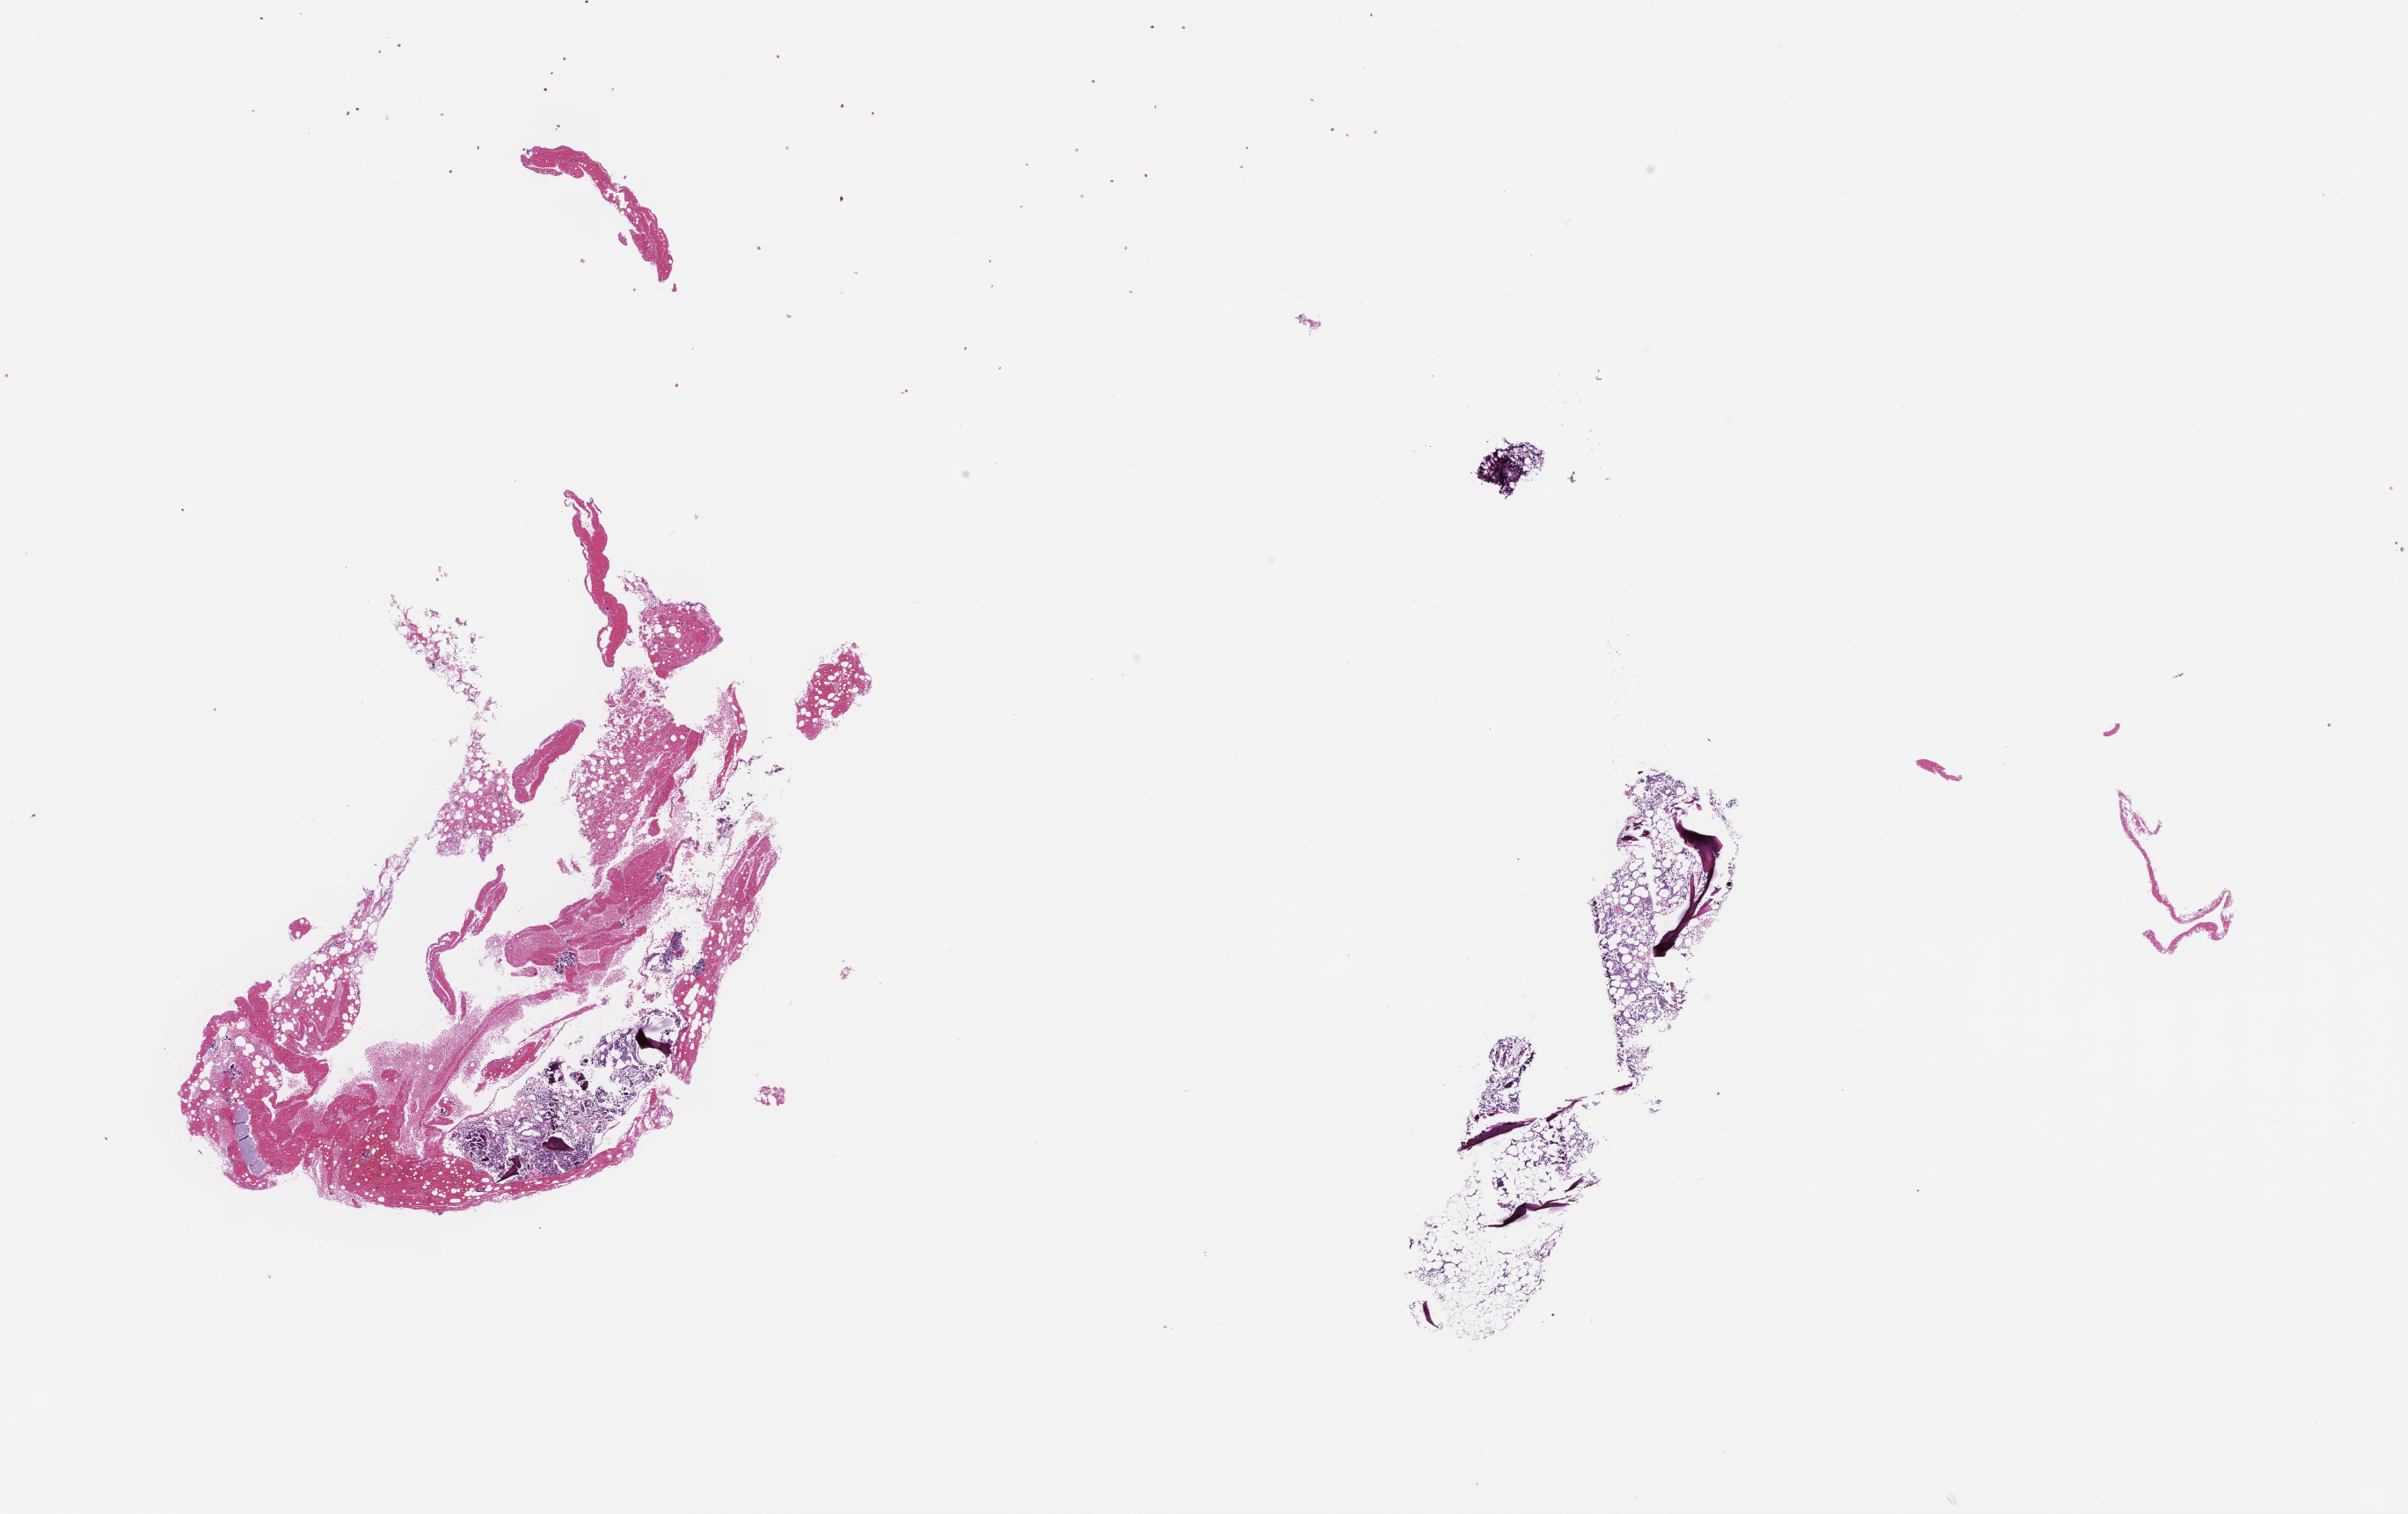
Digitized H&E-stained section — shown as a low-resolution overview of the whole scanned area (about 22.1 x 13.9 mm); formalin-fixed, paraffin-embedded (FFPE) tissue. Patient: male.
This section: metastasis (sampled organ not recorded). Patient diagnosis (primary): Plasma Cell Myeloma.